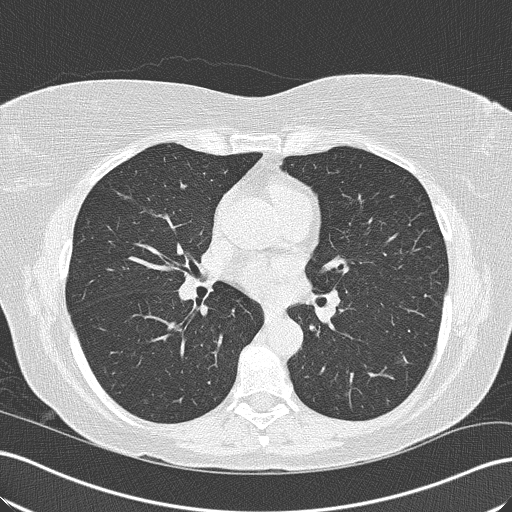
Chest CT (low-dose screening protocol), one axial image, second screening round (one year after baseline), lung window (W 1500 / L -600 HU), 2 mm slice thickness, lung (sharp) reconstruction kernel (B50f), slice 86 of 165 in the series, 512 × 512 image matrix, field of view 358 × 358 mm. Female, age 57 years at enrolment. Current smoker at enrolment.
Expert reader's lesion annotation, bounding box (x1, y1, x2, y2) in pixels: (376, 341, 431, 388). The screening reader recorded 6 non-calcified nodules or masses ≥4 mm on this exam (left lower lobe, right upper lobe, right upper lobe, right upper lobe, right lower lobe, right upper lobe); which of them this box marks is not recorded. Official screen result: positive, no significant change: stable abnormalities potentially related to lung cancer, unchanged since the prior screening exam. Later outcome: lung cancer diagnosed 482 days after this screen — bronchiolo-alveolar adenocarcinoma, NOS, left lower lobe, well differentiated (G1), stage IA (AJCC 6th edition), 16 mm at pathology.